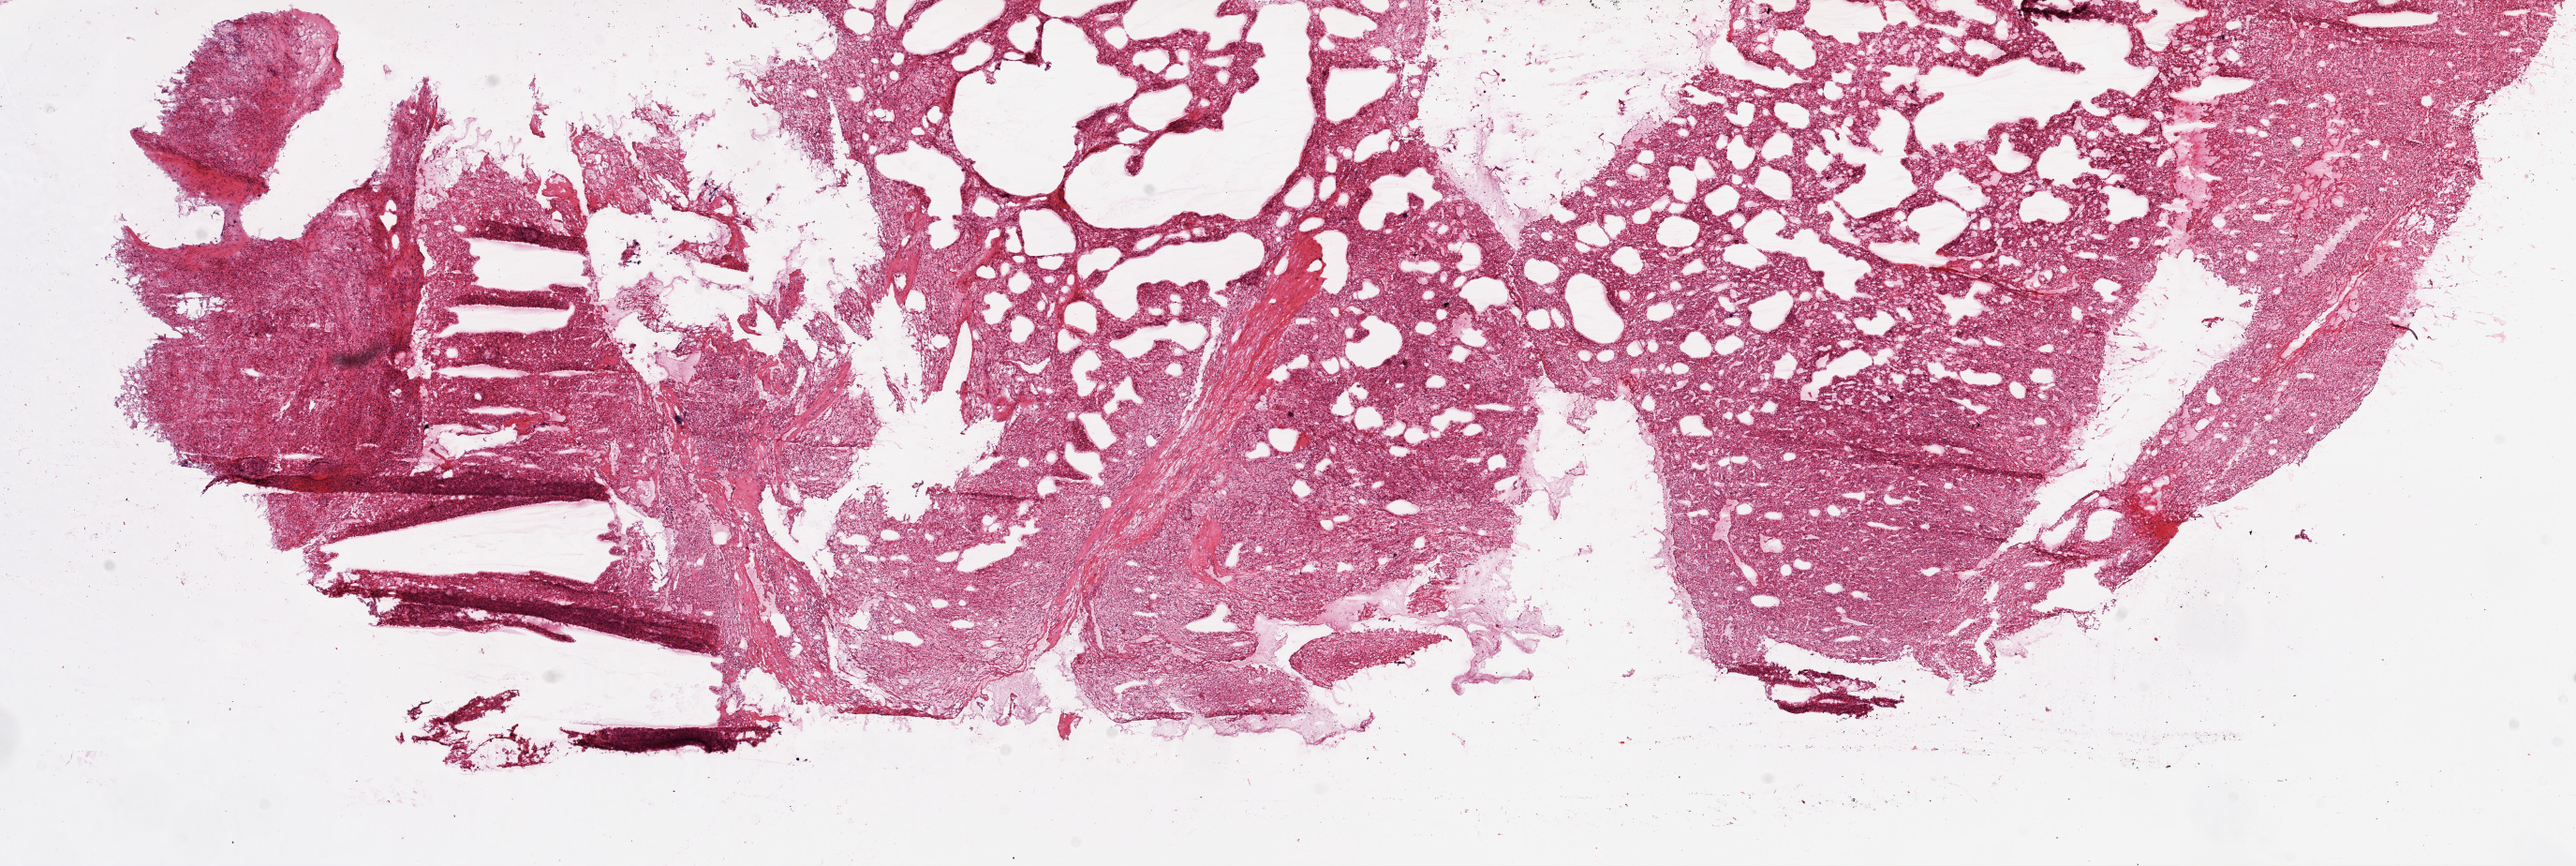
Whole-slide histology image, H&E-stained, a low-resolution overview of the entire scanned area, about 22.1 x 7.4 mm, frozen section from the top of the tissue portion, primary tumour sample from the kidney. Female, age 88 years at initial diagnosis. Histologic grade: G3 (poorly differentiated). Pathologist review of this section (percent, as recorded): tumour cells 85%, tumour nuclei 85%, normal cells 0%, stromal cells 15%, necrosis 0%.
Diagnosis: Clear cell adenocarcinoma, NOS. Laterality: right. TNM: T3b NX M0. AJCC pathologic stage: III.